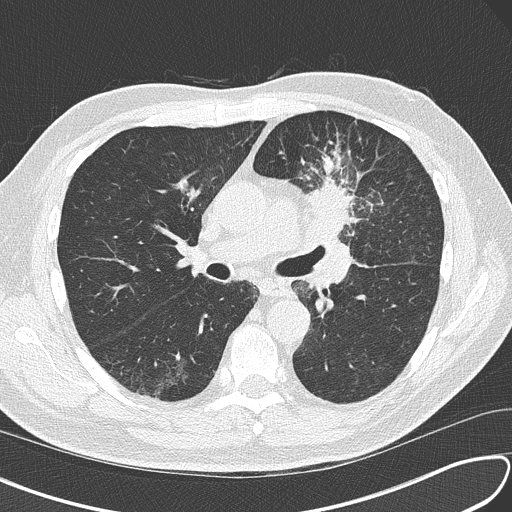
Low-dose screening chest CT, axial slice, third screening round (two years after baseline), lung window (W 1500 / L -600 HU), slice 66 of 156 in the series. Male participant, aged 67 years at enrolment.
Expert reader's lesion annotation, bounding box [x1, y1, x2, y2] px = [294, 159, 394, 249]. The exam's reader record, not a measurement of the box and not confirmed to be the same lesion: non-calcified nodule or mass ≥4 mm, left upper lobe, 30 × 23 mm, soft tissue attenuation, pre-existing on the prior screen: no. Participant outcome: lung cancer diagnosed 41 days after this screen — small cell carcinoma, NOS, left upper lobe, stage IV (AJCC 6th edition), 30 mm at pathology.